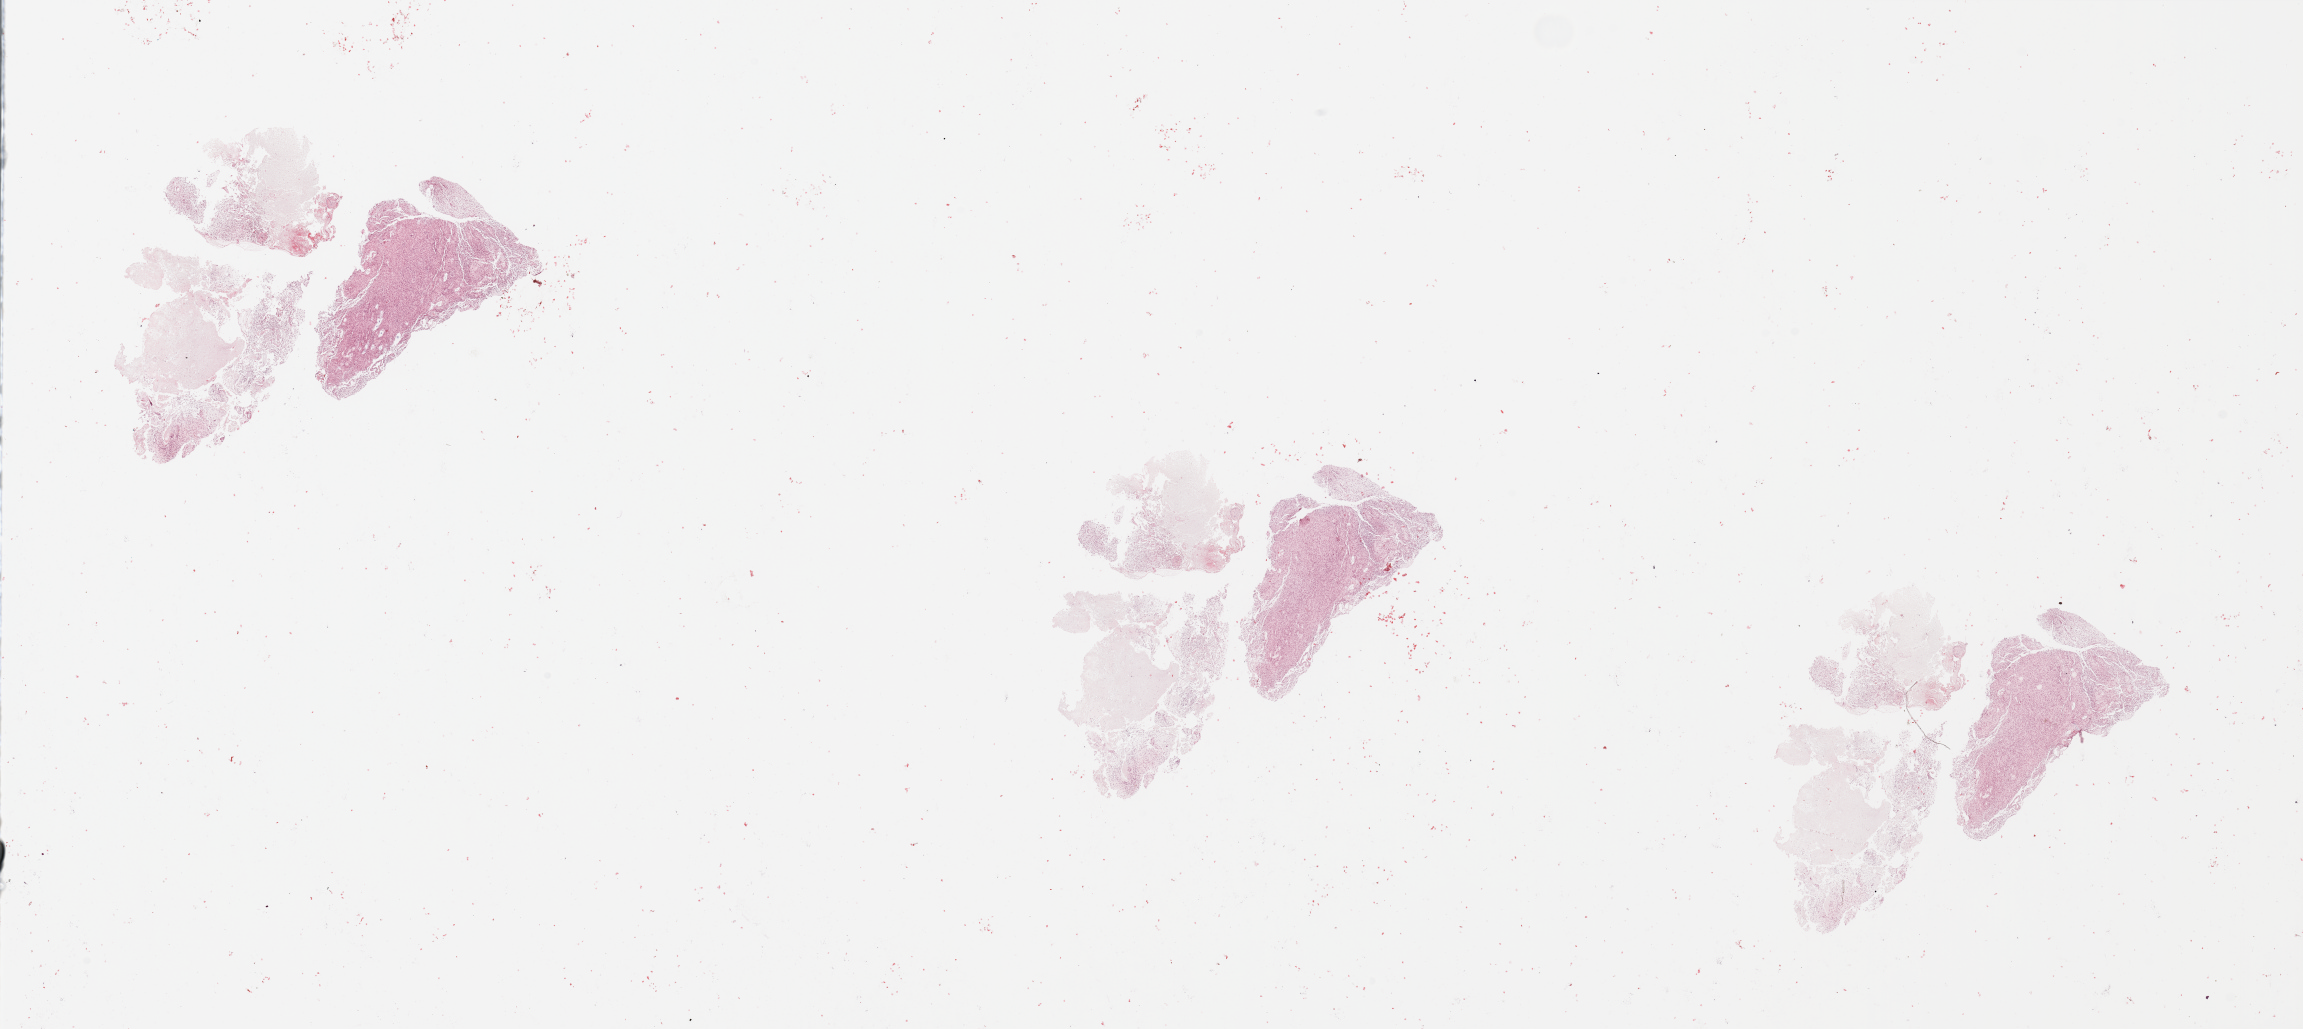
H&E whole-slide image — low-resolution overview of the scanned area, about 36.4 x 16.3 mm, tumour tissue sample, sampled site: brain. Male, 47 y/o. Composition of this section per pathologist review: tumour nuclei 65%, necrosis 30%.
Diagnosis: Glioblastoma. Primary tumour site (as recorded): left hemisphere.